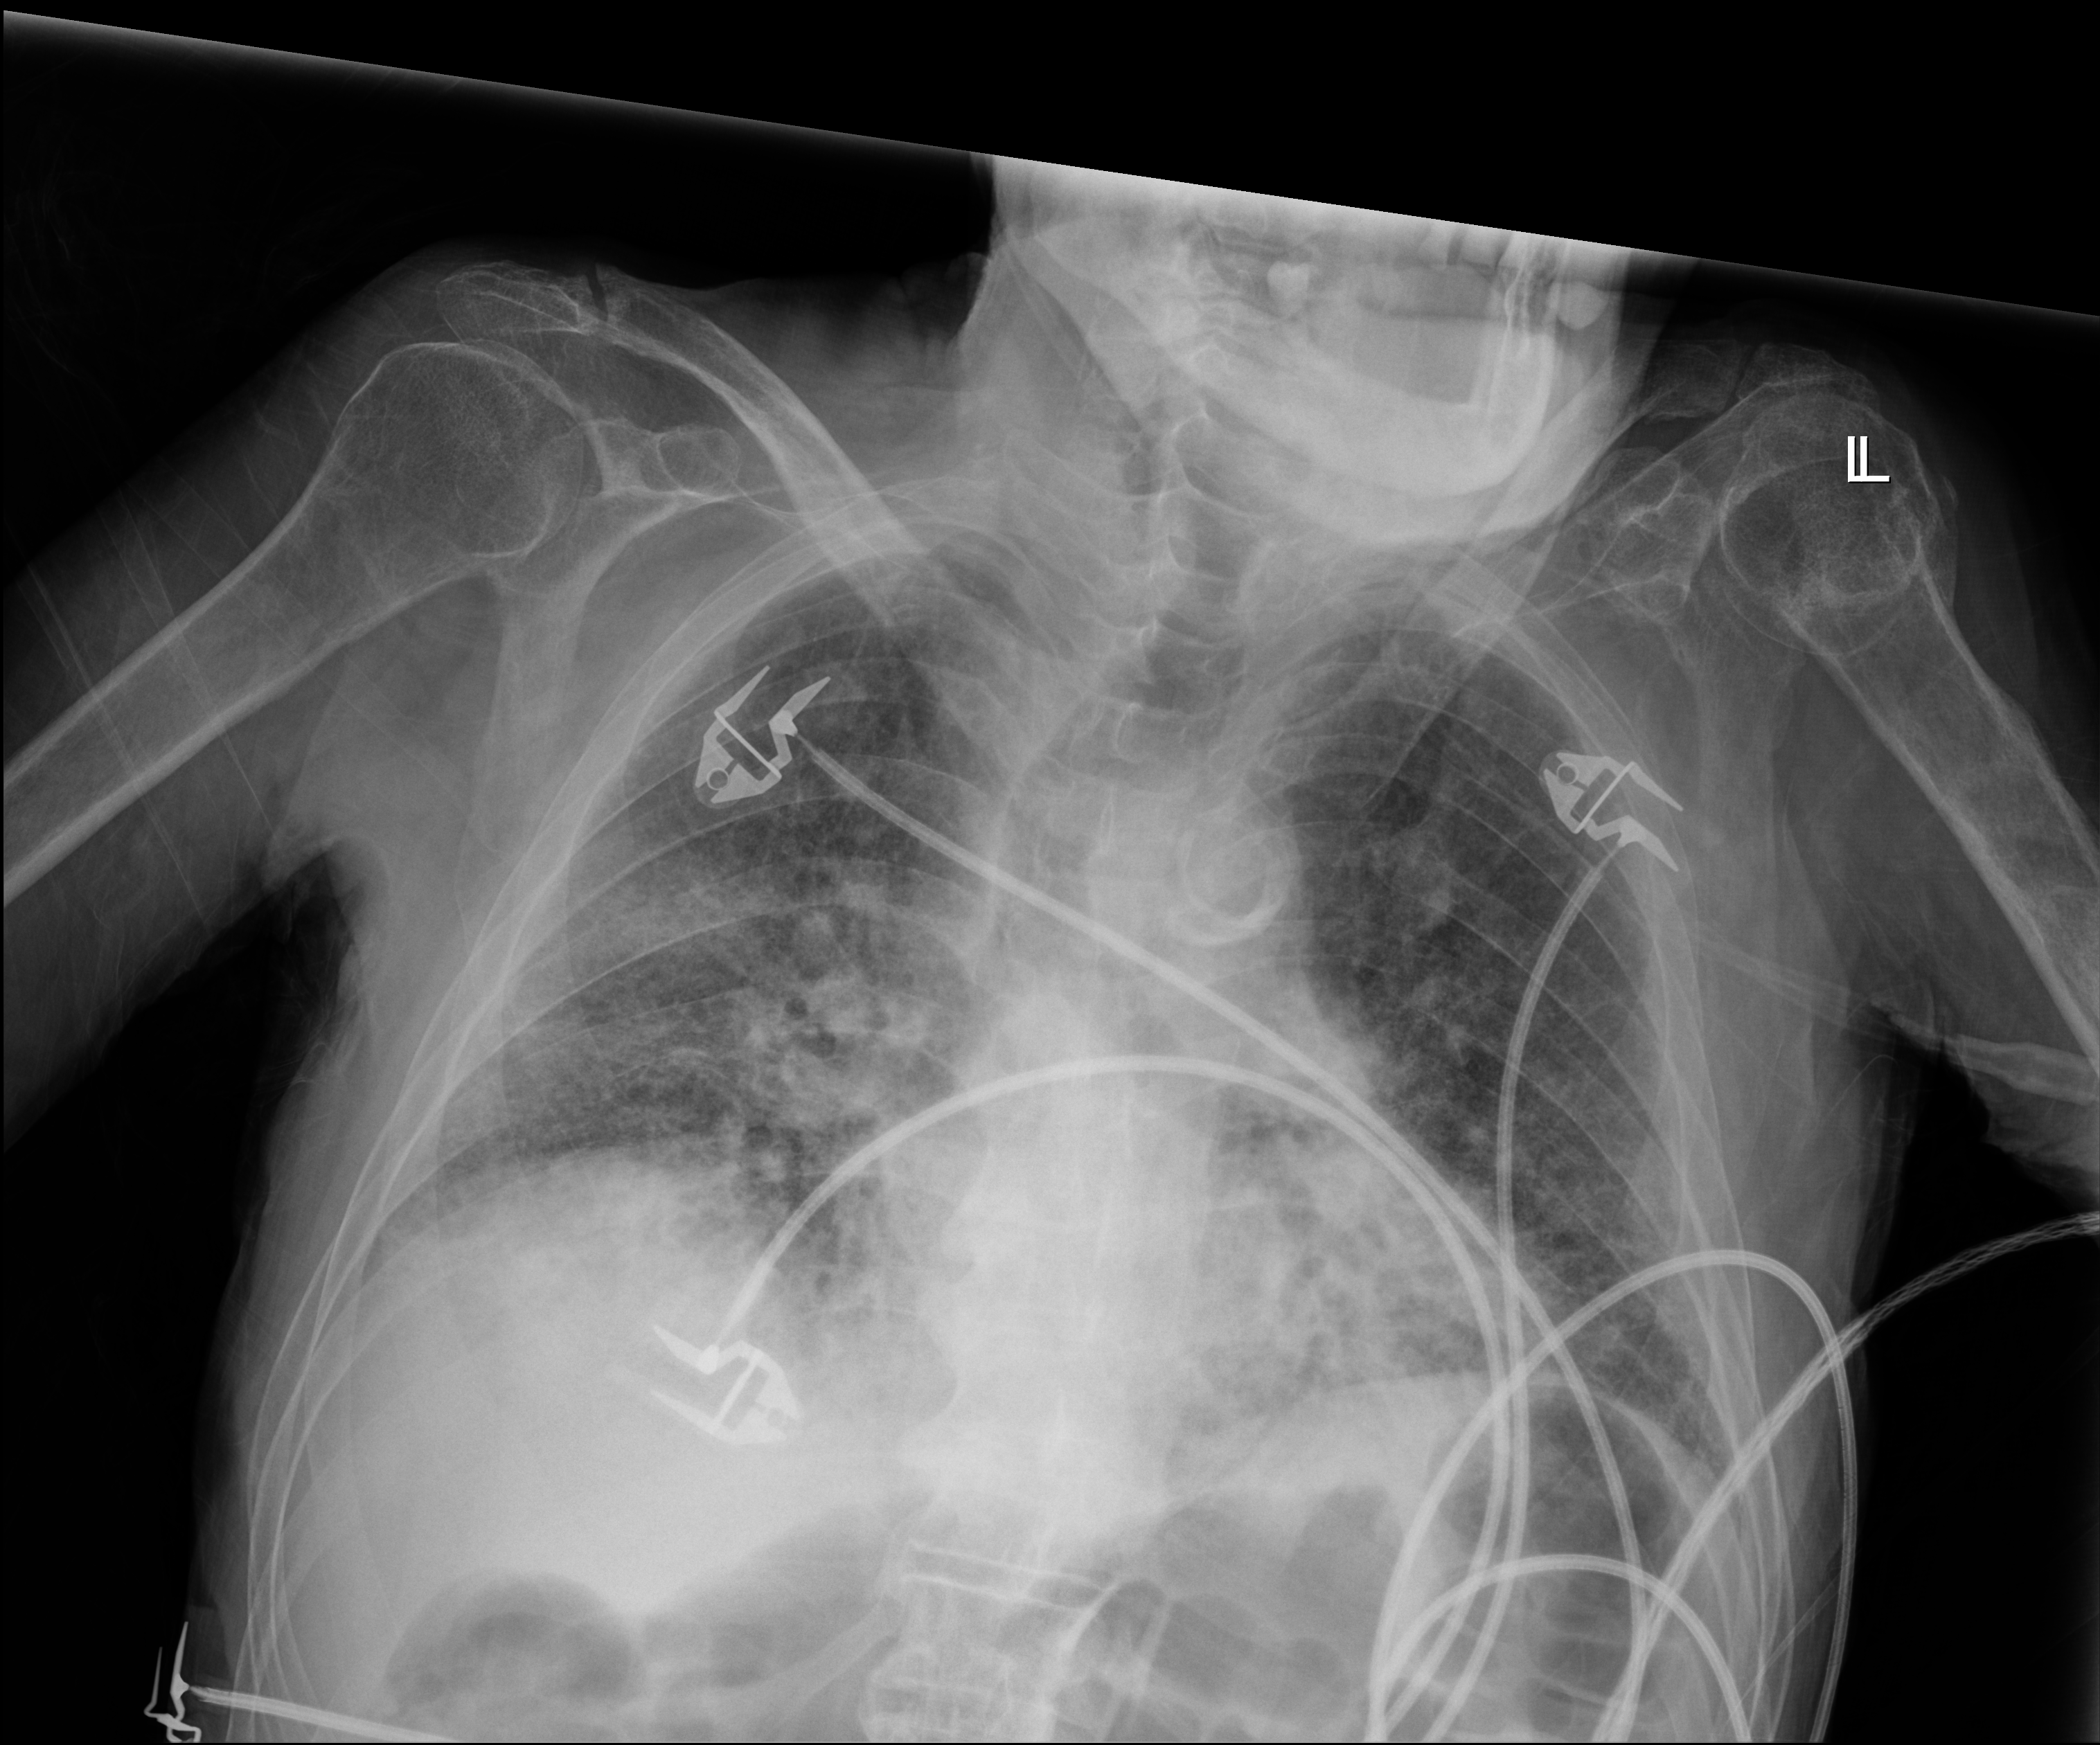
Chest radiograph (digital radiography); anteroposterior (AP) projection. Patient hospitalised with COVID-19; male, aged 60–74 years.
Hospital-stay facts (about this admission, not read from this image; timing relative to this image not recorded):
- mechanically ventilated during this hospital stay: no
- admitted to intensive care during this hospital stay: no